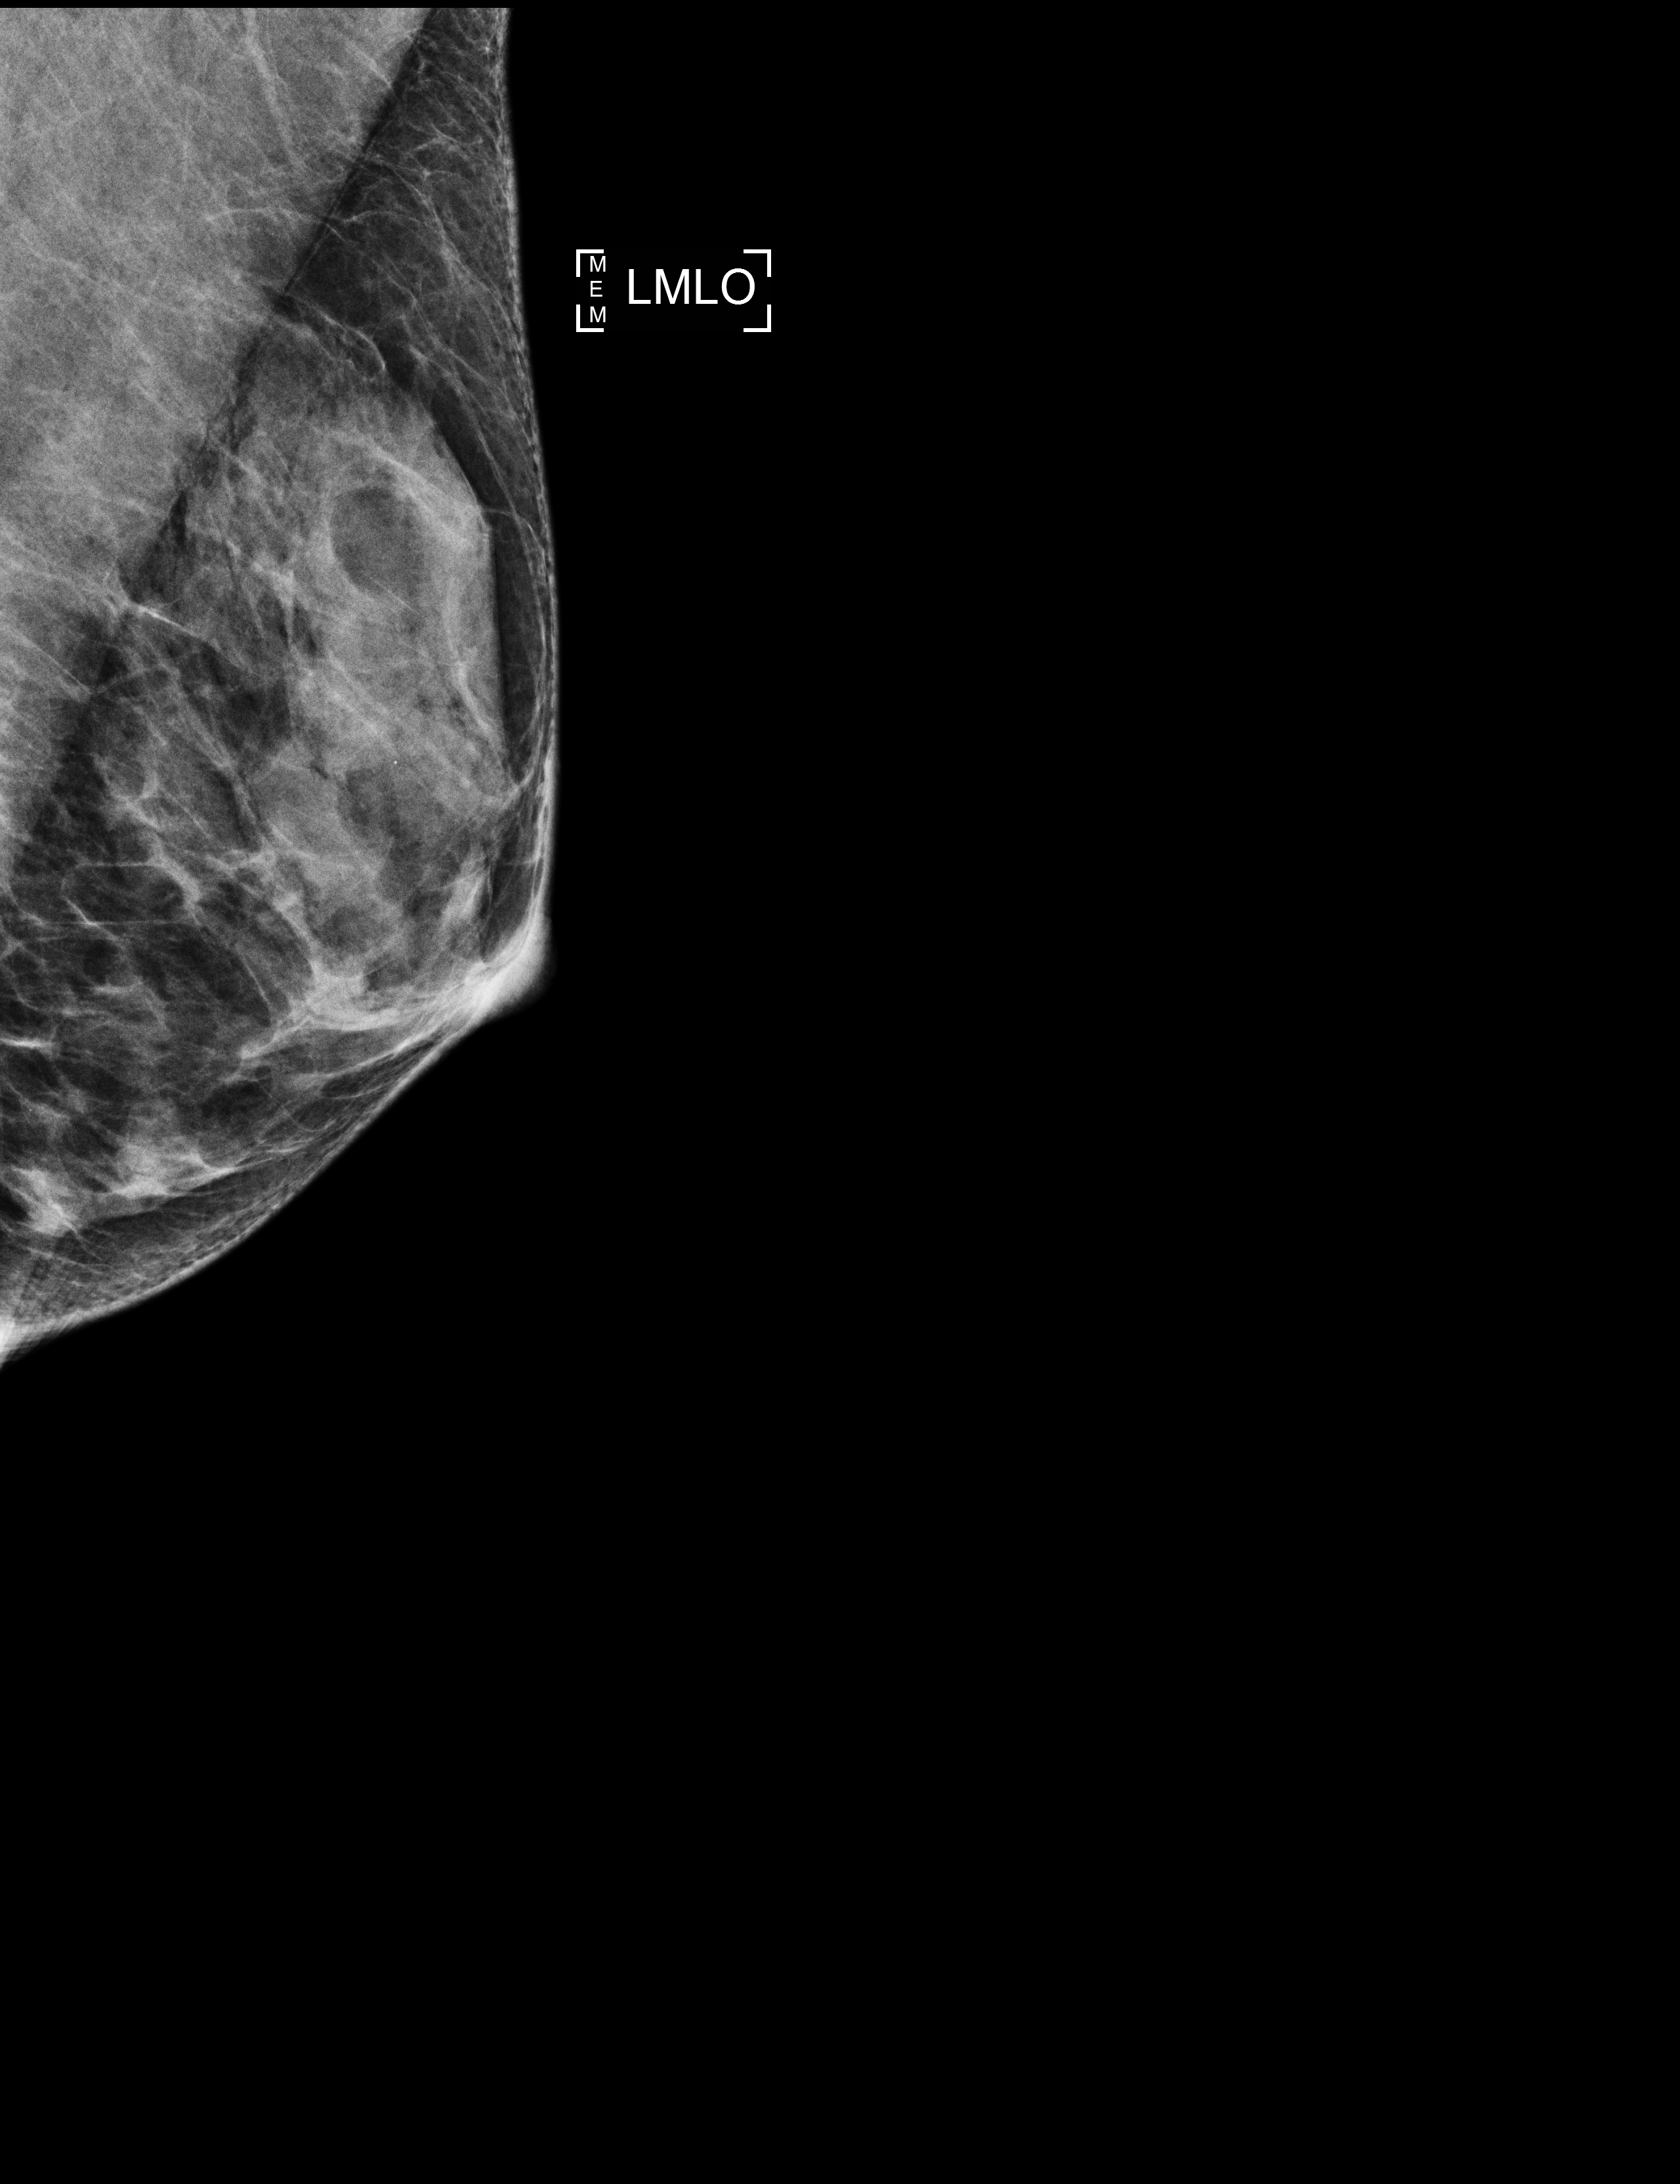
Annual screening mammography examination, compressed breast thickness 22 mm. Patient aged 60 years (female).
Image type: full-field digital mammogram. Breast: left. Projection: mediolateral oblique (MLO) view. Breast density at the screening exam (both breasts): heterogeneously dense (BI-RADS density category c). Final BI-RADS assessment for this screening round (tomosynthesis exam, both breasts): category 1. Recall: no recall after this screen.